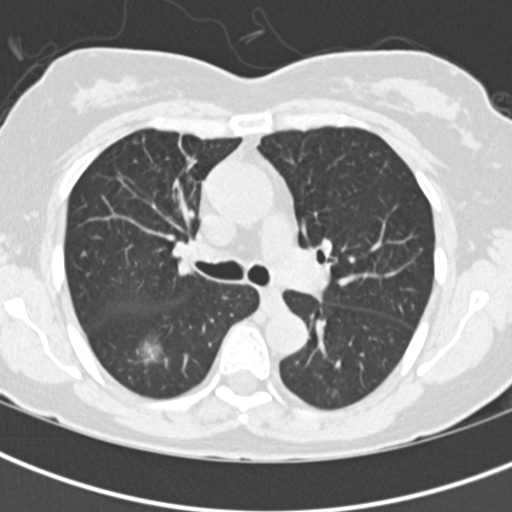
Low-dose screening chest CT, one axial slice; slice 135 of 198 in the series (ordered by position); reconstruction kernel B30f; lung window (W 1500 / L -600 HU); 512 × 512 image matrix.
Structures marked on this image (manually delineated by an expert):
- lesion 1 (tumor, lower lobe of right lung): bounding box <137,337,163,364> (left, top, right, bottom; pixels)